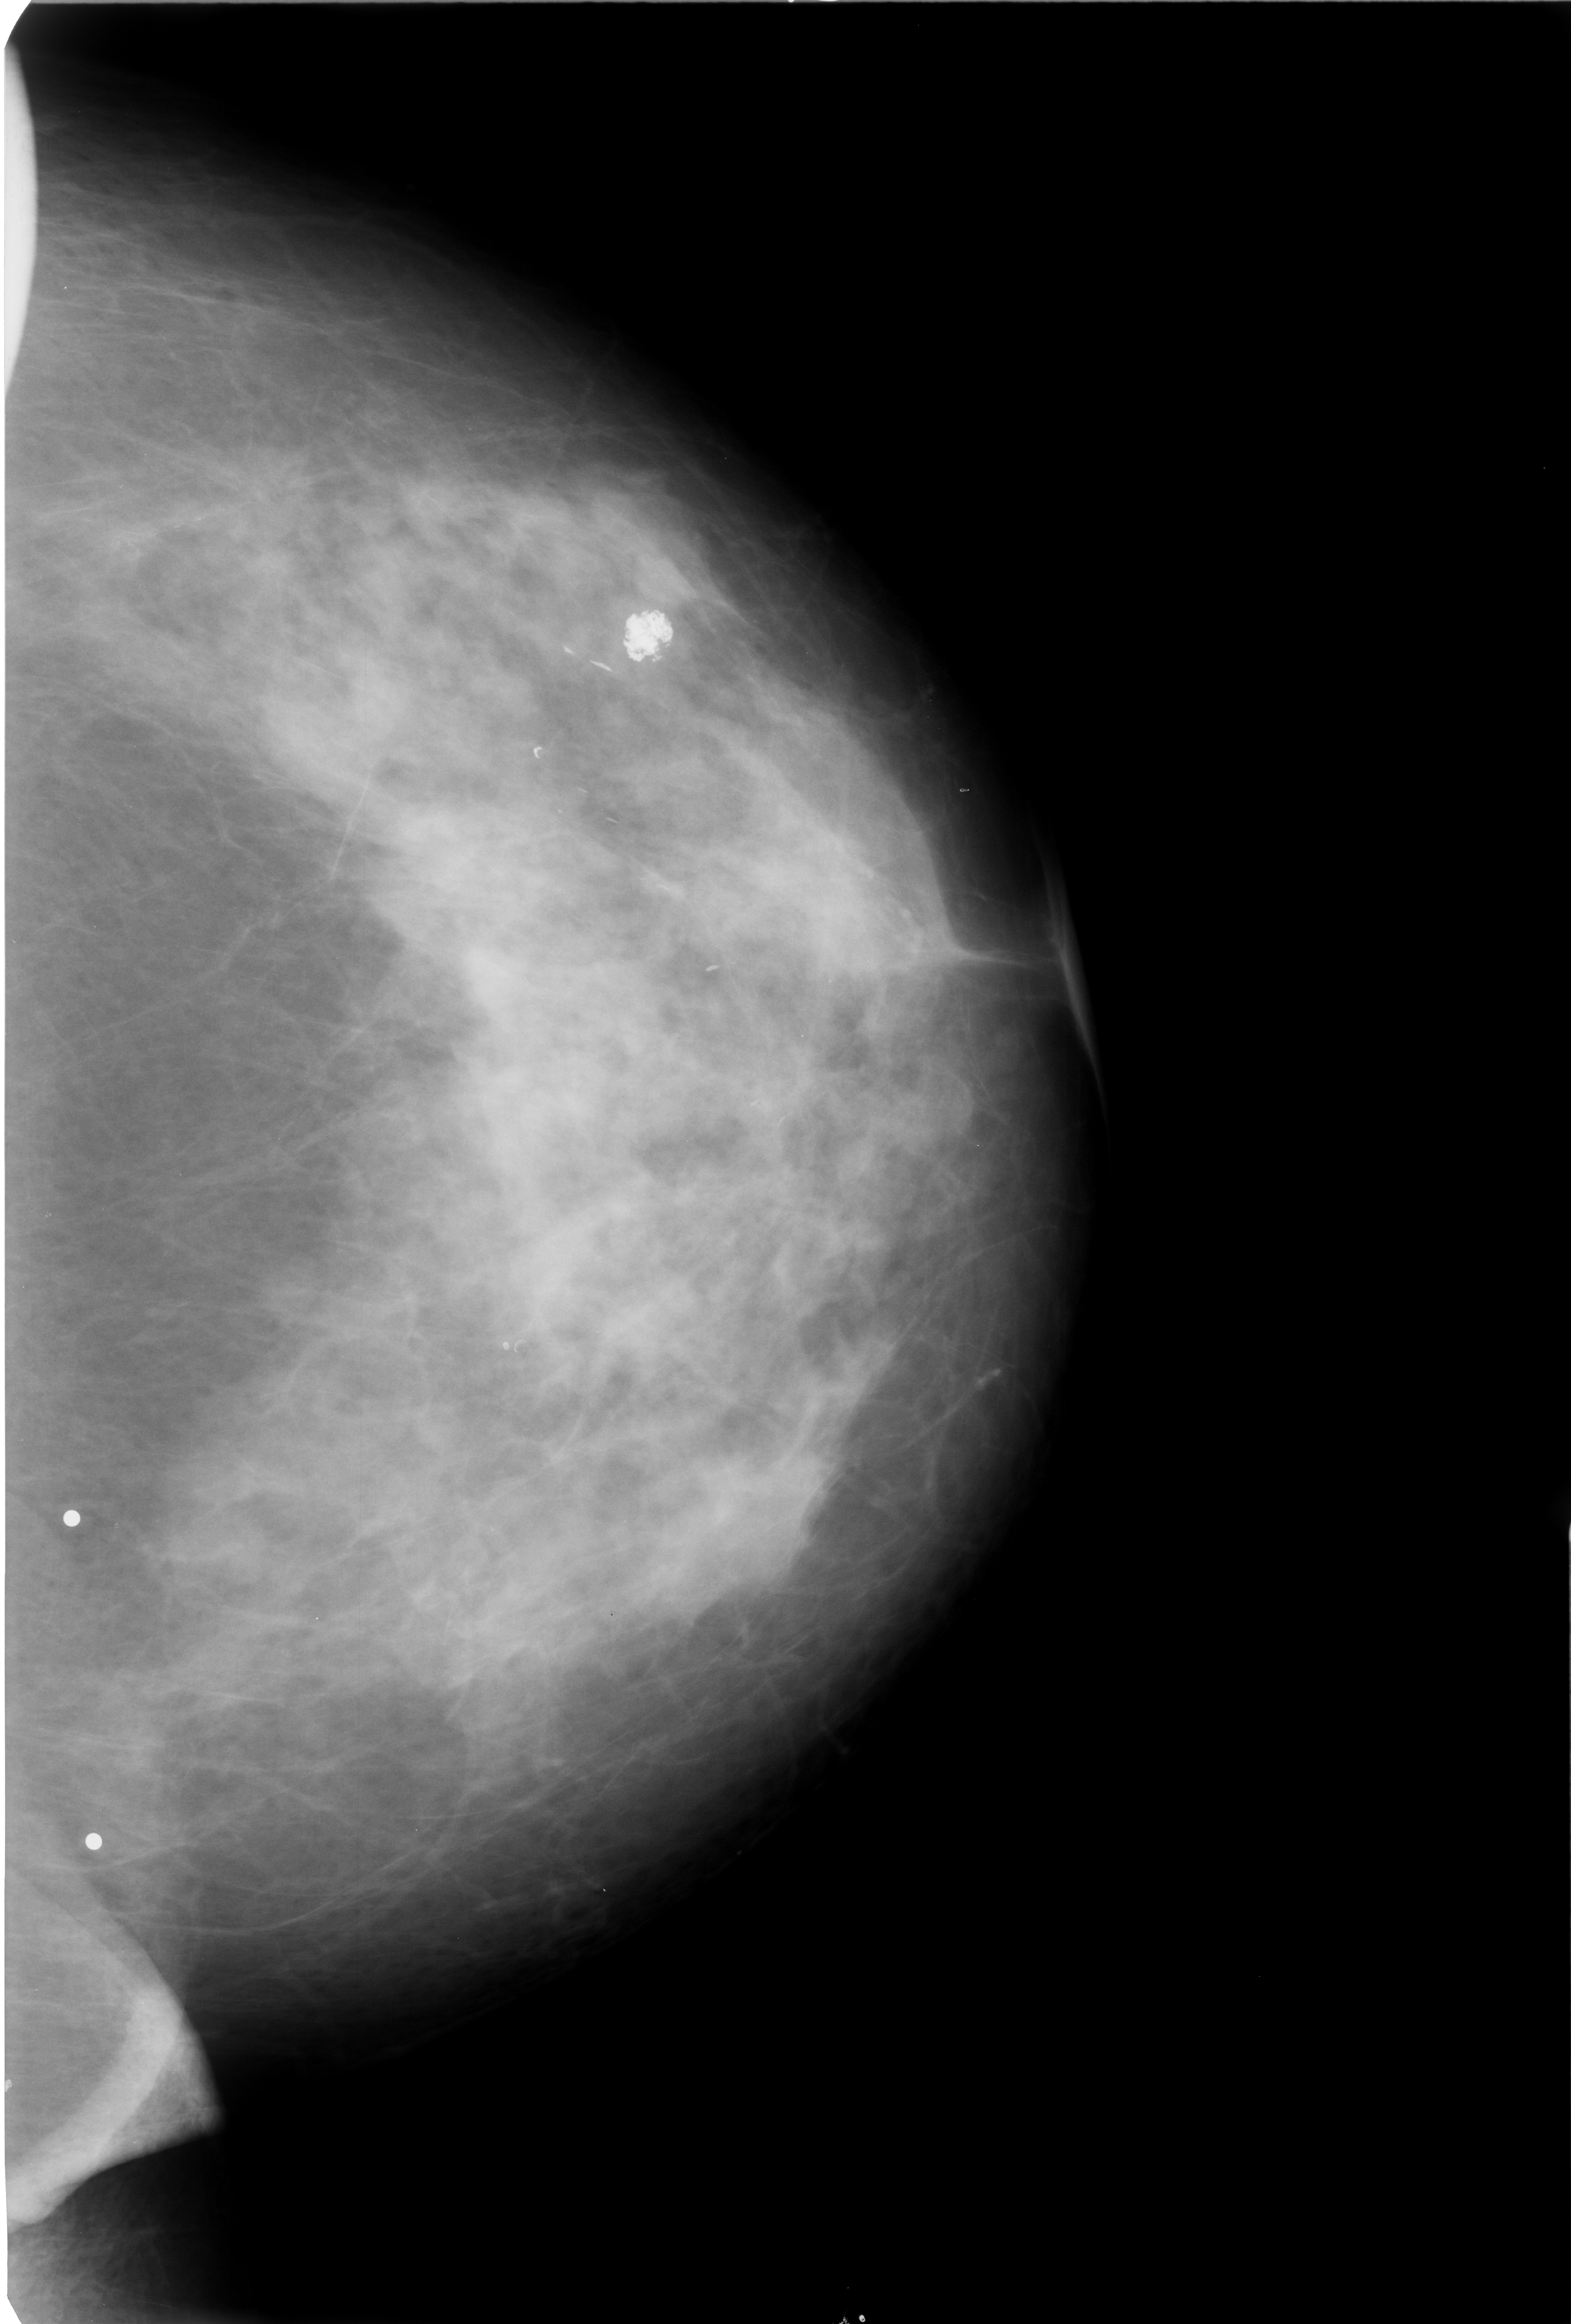
Digitized screen-film mammogram; left breast; craniocaudal (CC) view.
Radiologist-marked abnormalities on this image: calcifications, distribution linear; BI-RADS assessment category 2; subtlety rating 3 on a 1 (subtle) to 5 (obvious) scale; benign; no additional work-up was recommended (benign without callback).